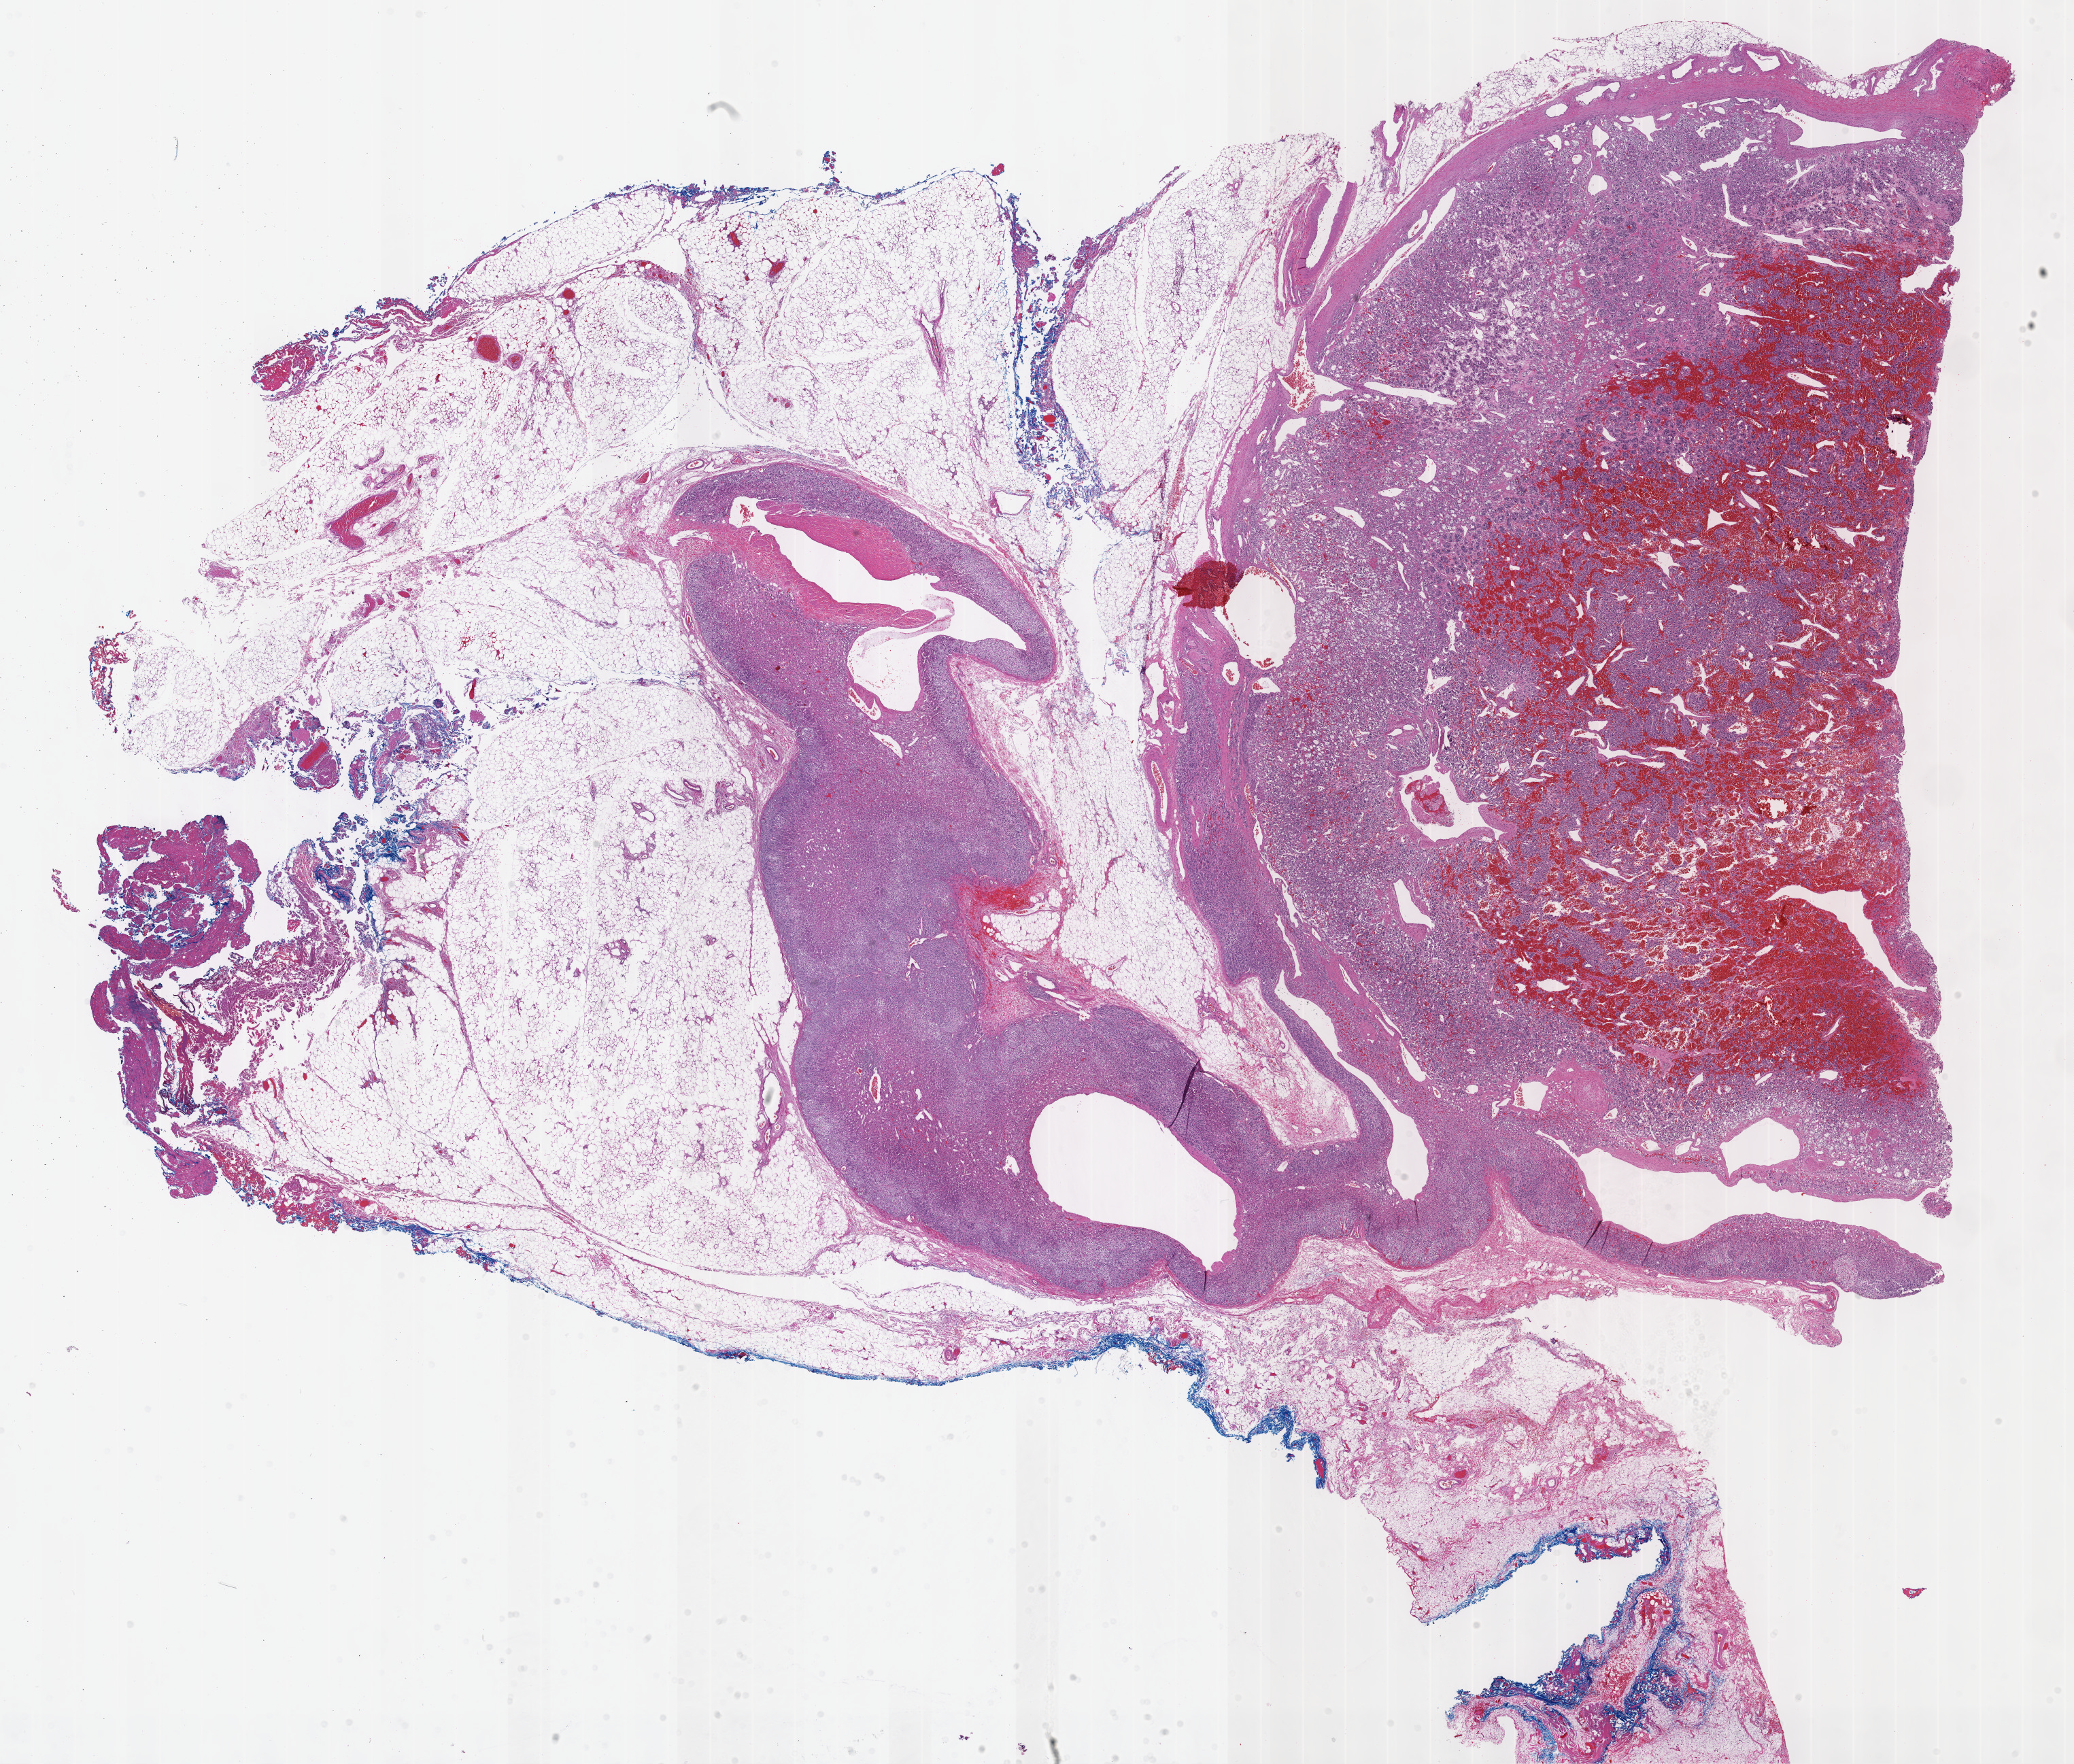
H&E-stained whole-slide image — low-resolution overview of the scanned area, about 24.7 x 21.0 mm (slide scanned at 40x); formalin-fixed paraffin-embedded (FFPE) diagnostic section; adrenal gland, primary tumour sample. Female patient; age at initial diagnosis 30 years.
Pathologic diagnosis: Pheochromocytoma, NOS.